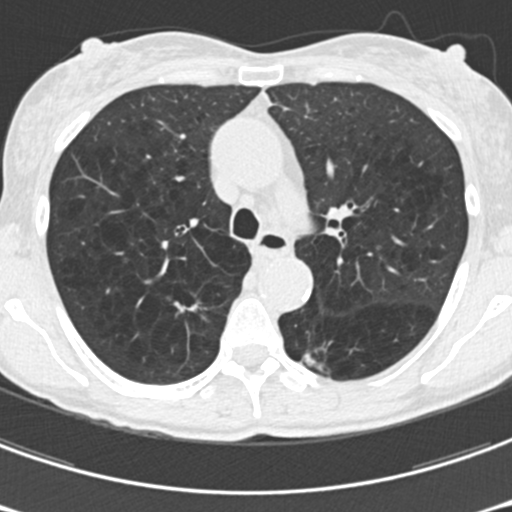
Low-dose screening chest CT, one axial slice; position 119 of 176 along the scan axis; lung window (W 1500 / L -600 HU); 512 × 512 image matrix.
Structures marked on this image (manually delineated by an expert):
- lesion 1 (tumor, upper lobe of right lung): box from (x=175, y=302) to (x=197, y=312) px